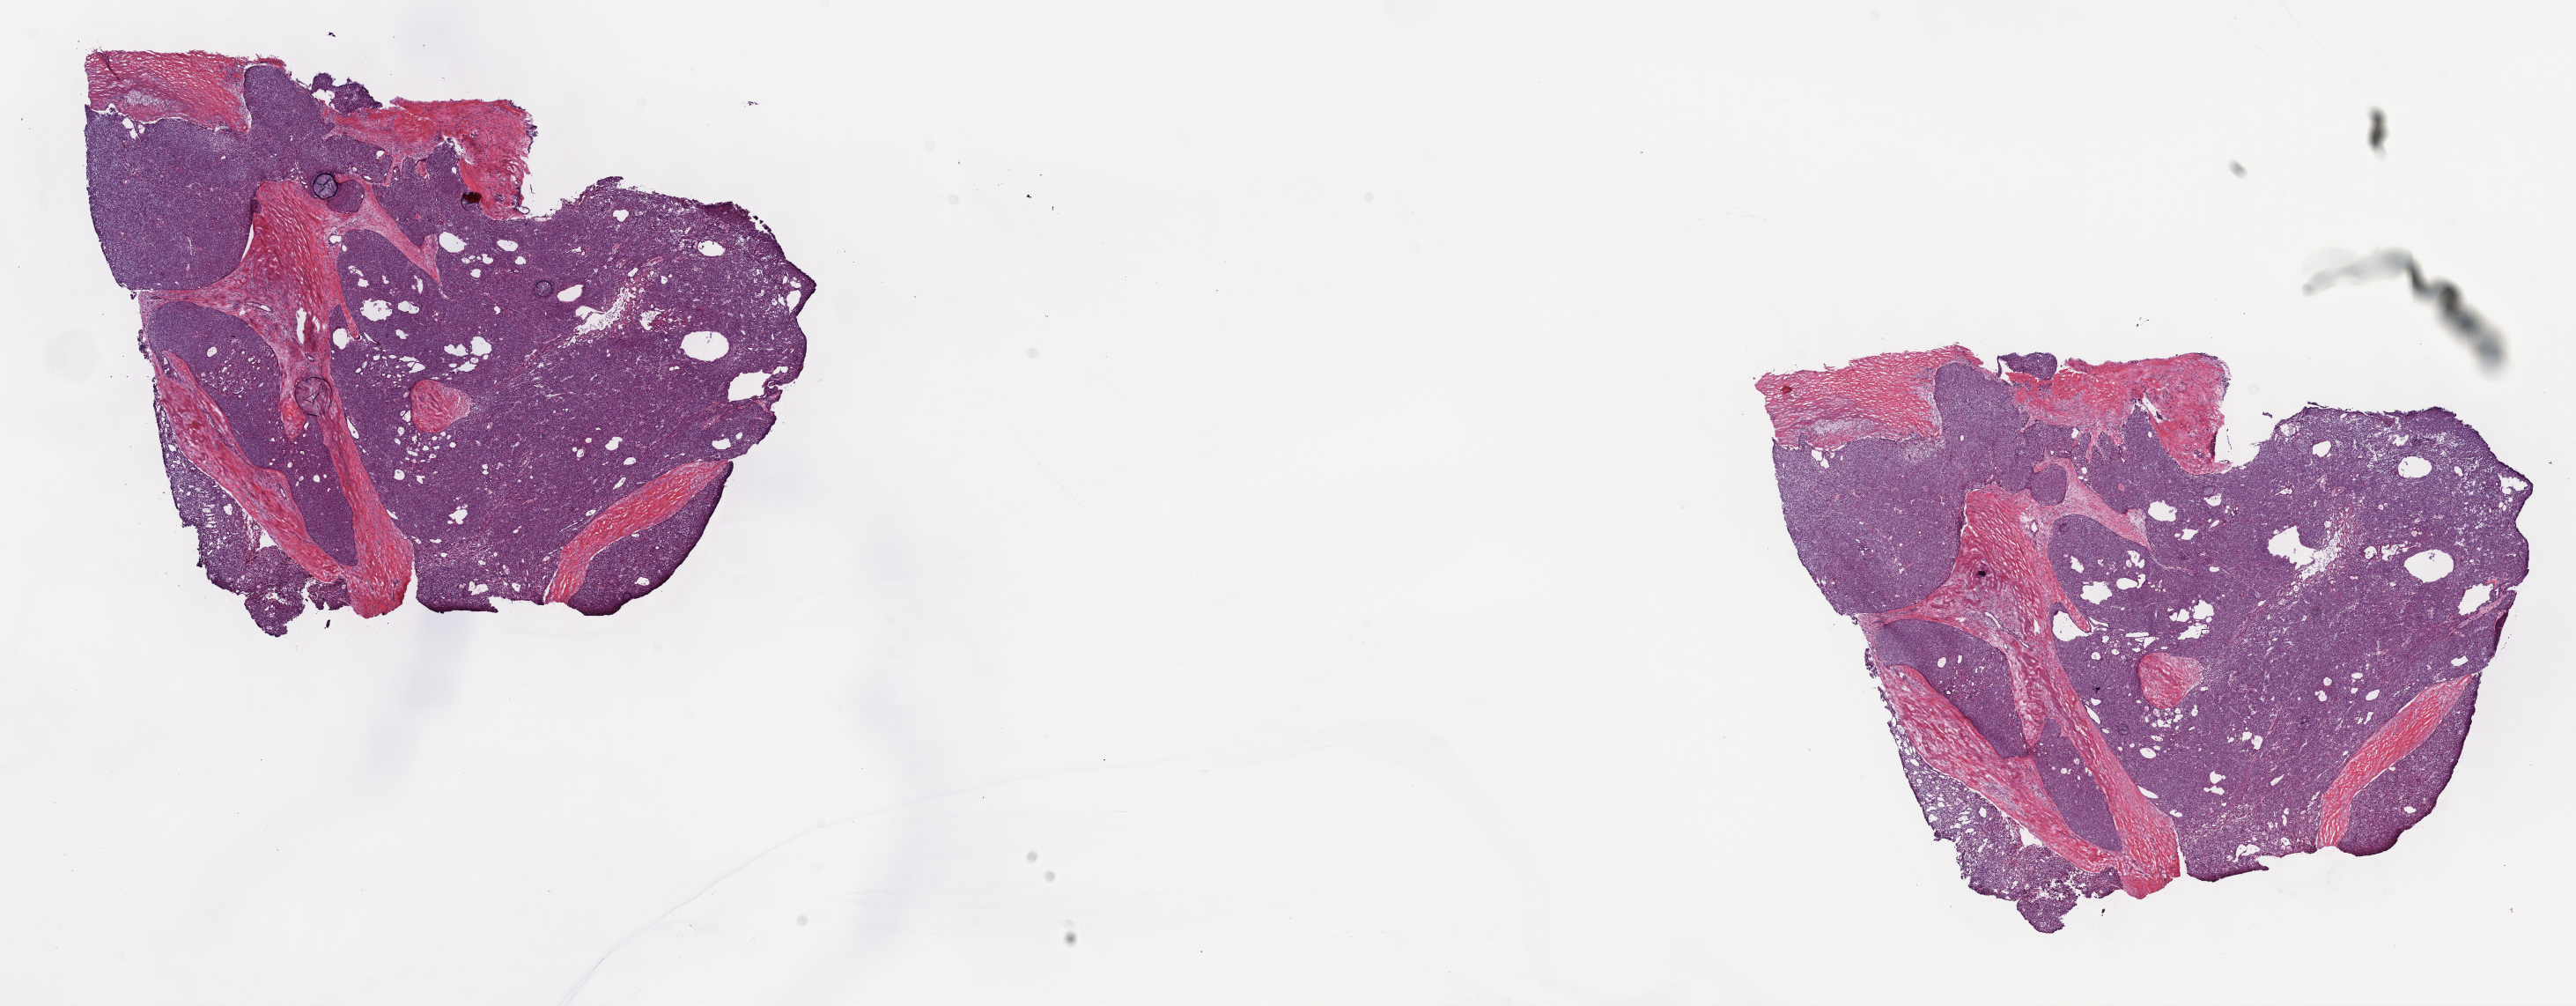
Hematoxylin and eosin (H&E) stained whole-slide image, whole scanned area (about 23.7 x 9.2 mm, acquisition: 40x scan) shown as a low-resolution overview; frozen section; thymus, primary tumour sample. Male, age 73 years at initial diagnosis. Pathologist review of this section (percent, as recorded): tumour cells 70%, tumour nuclei 90%, normal cells 0%, stromal cells 30%, necrosis 0%. Infiltration values recorded for this section: lymphocyte infiltration 0%, monocyte infiltration 0%, neutrophil infiltration 0%.
Diagnosis: Thymoma, type A, malignant.